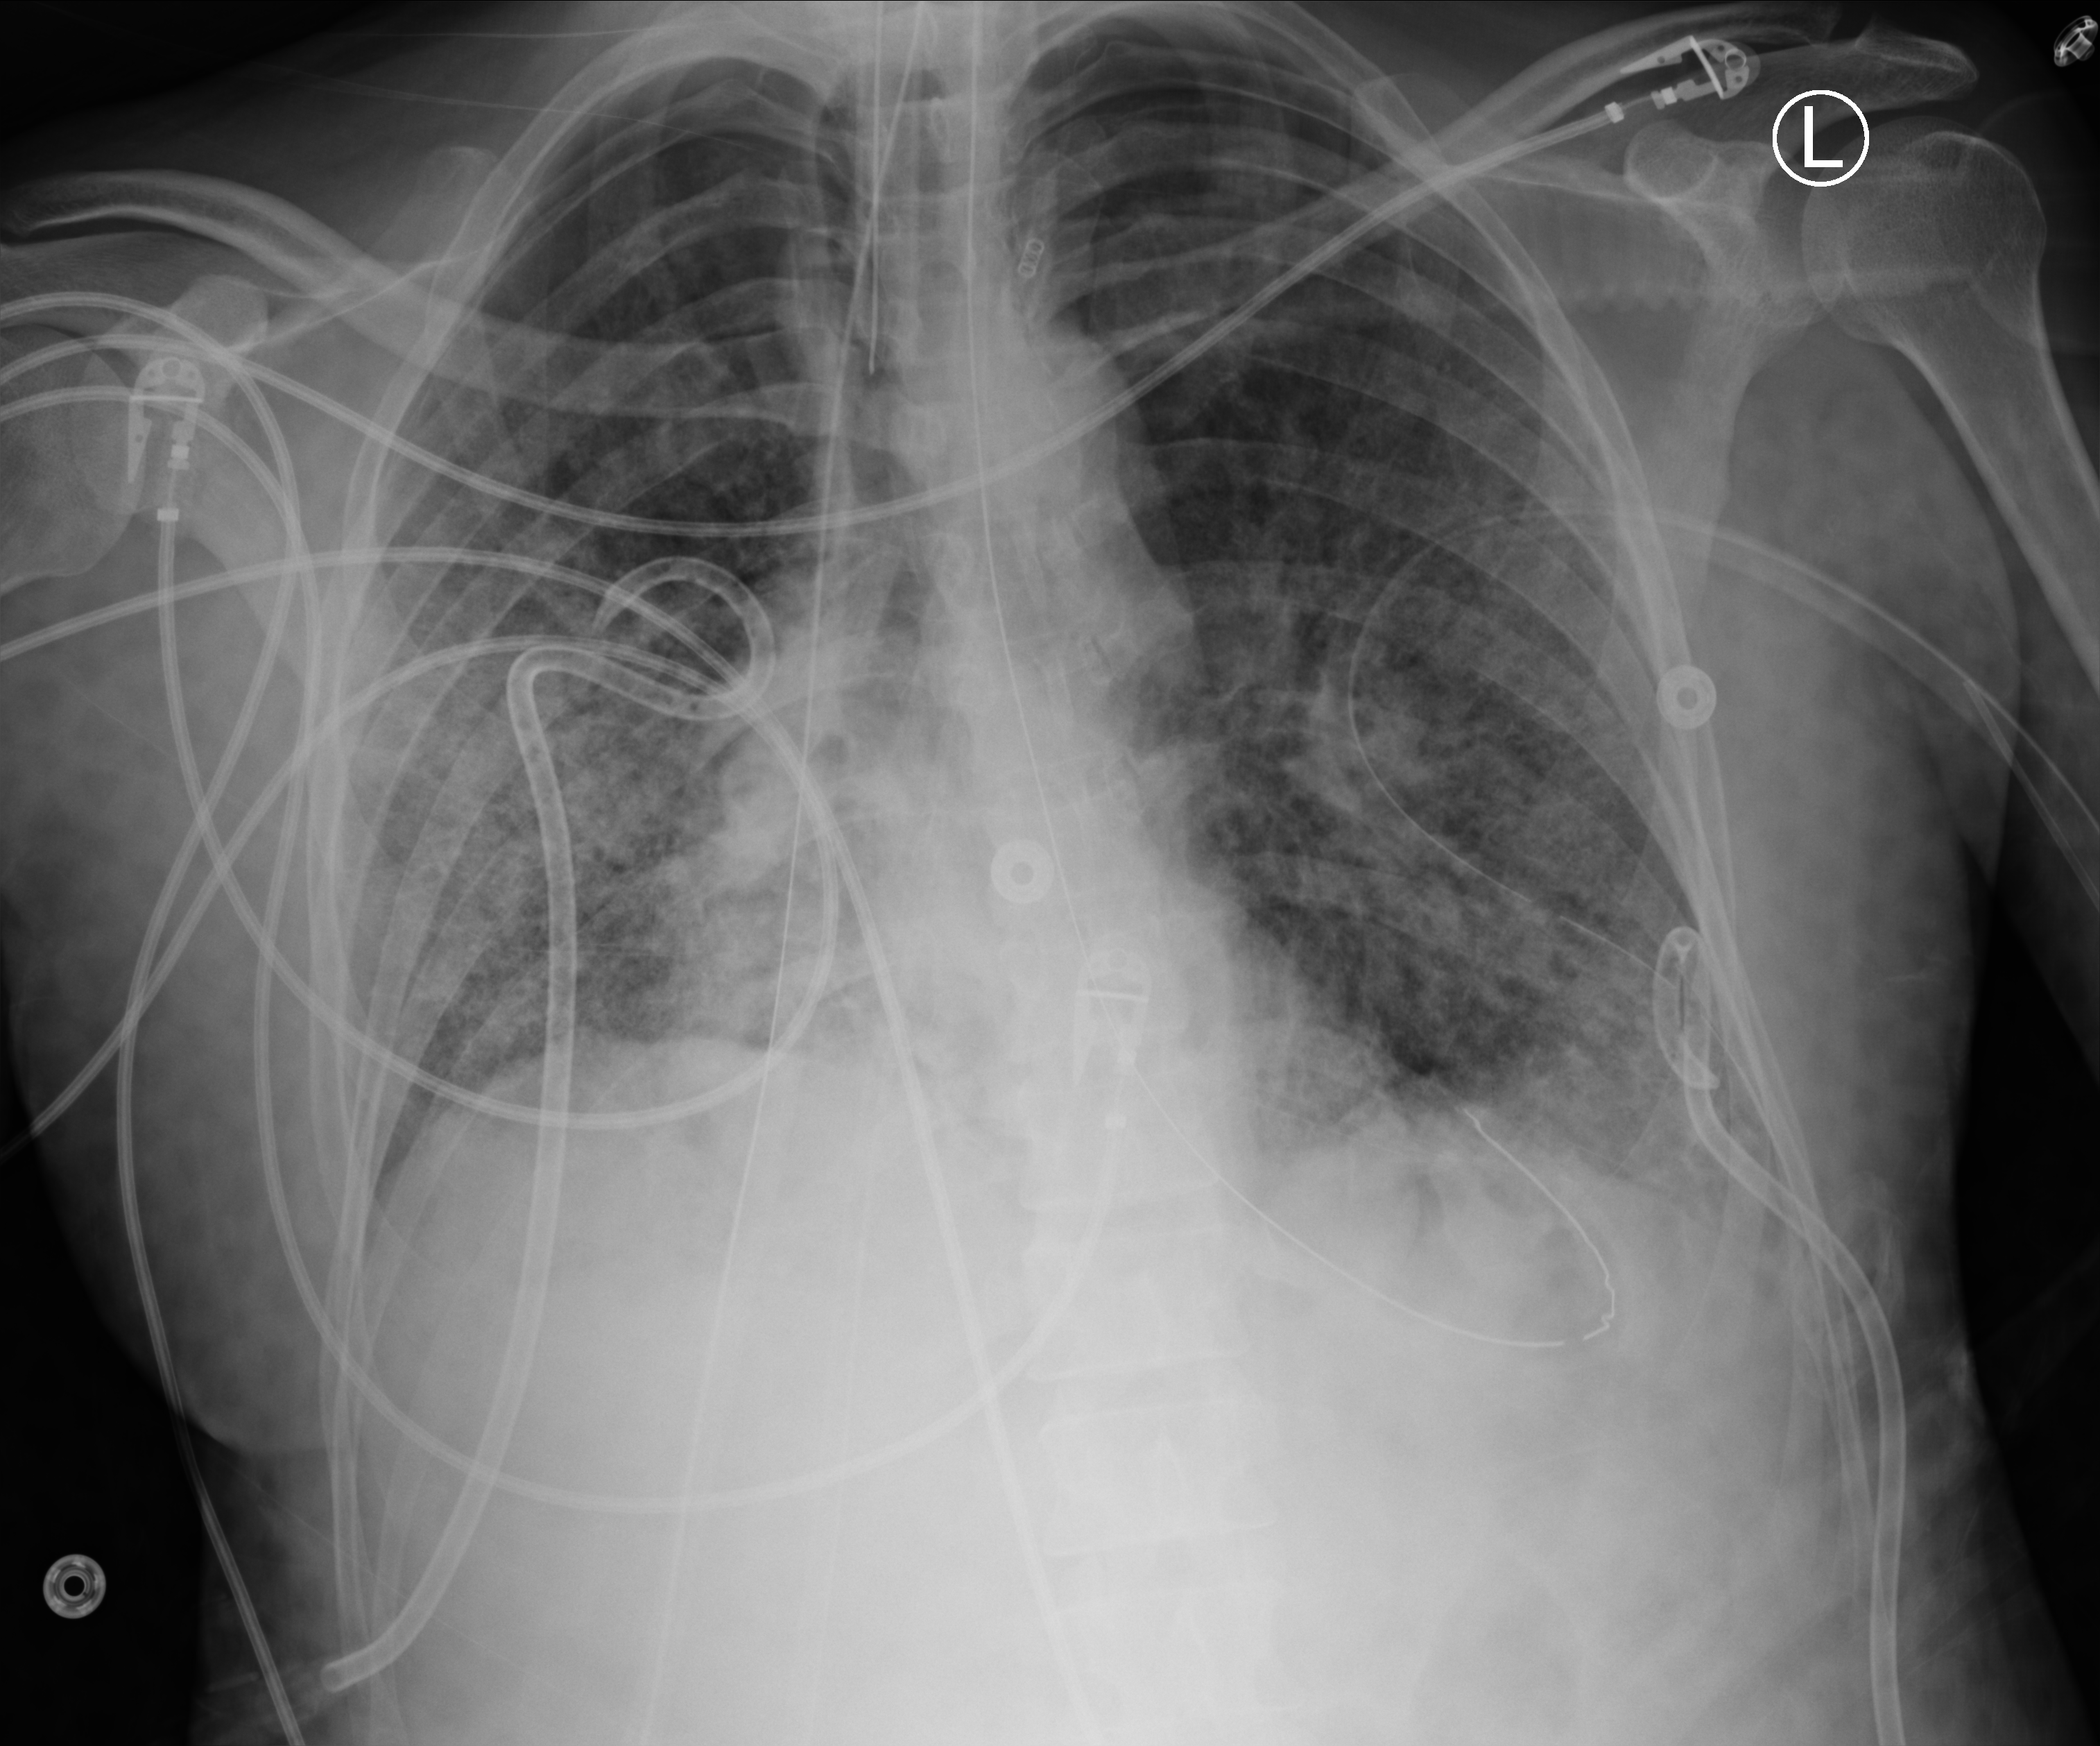
Portable chest radiograph. Patient hospitalised with COVID-19, aged 18–59 years.
Admission-level facts for this patient (not findings on this image; timing relative to this image not recorded):
- mechanically ventilated during this hospital stay: yes